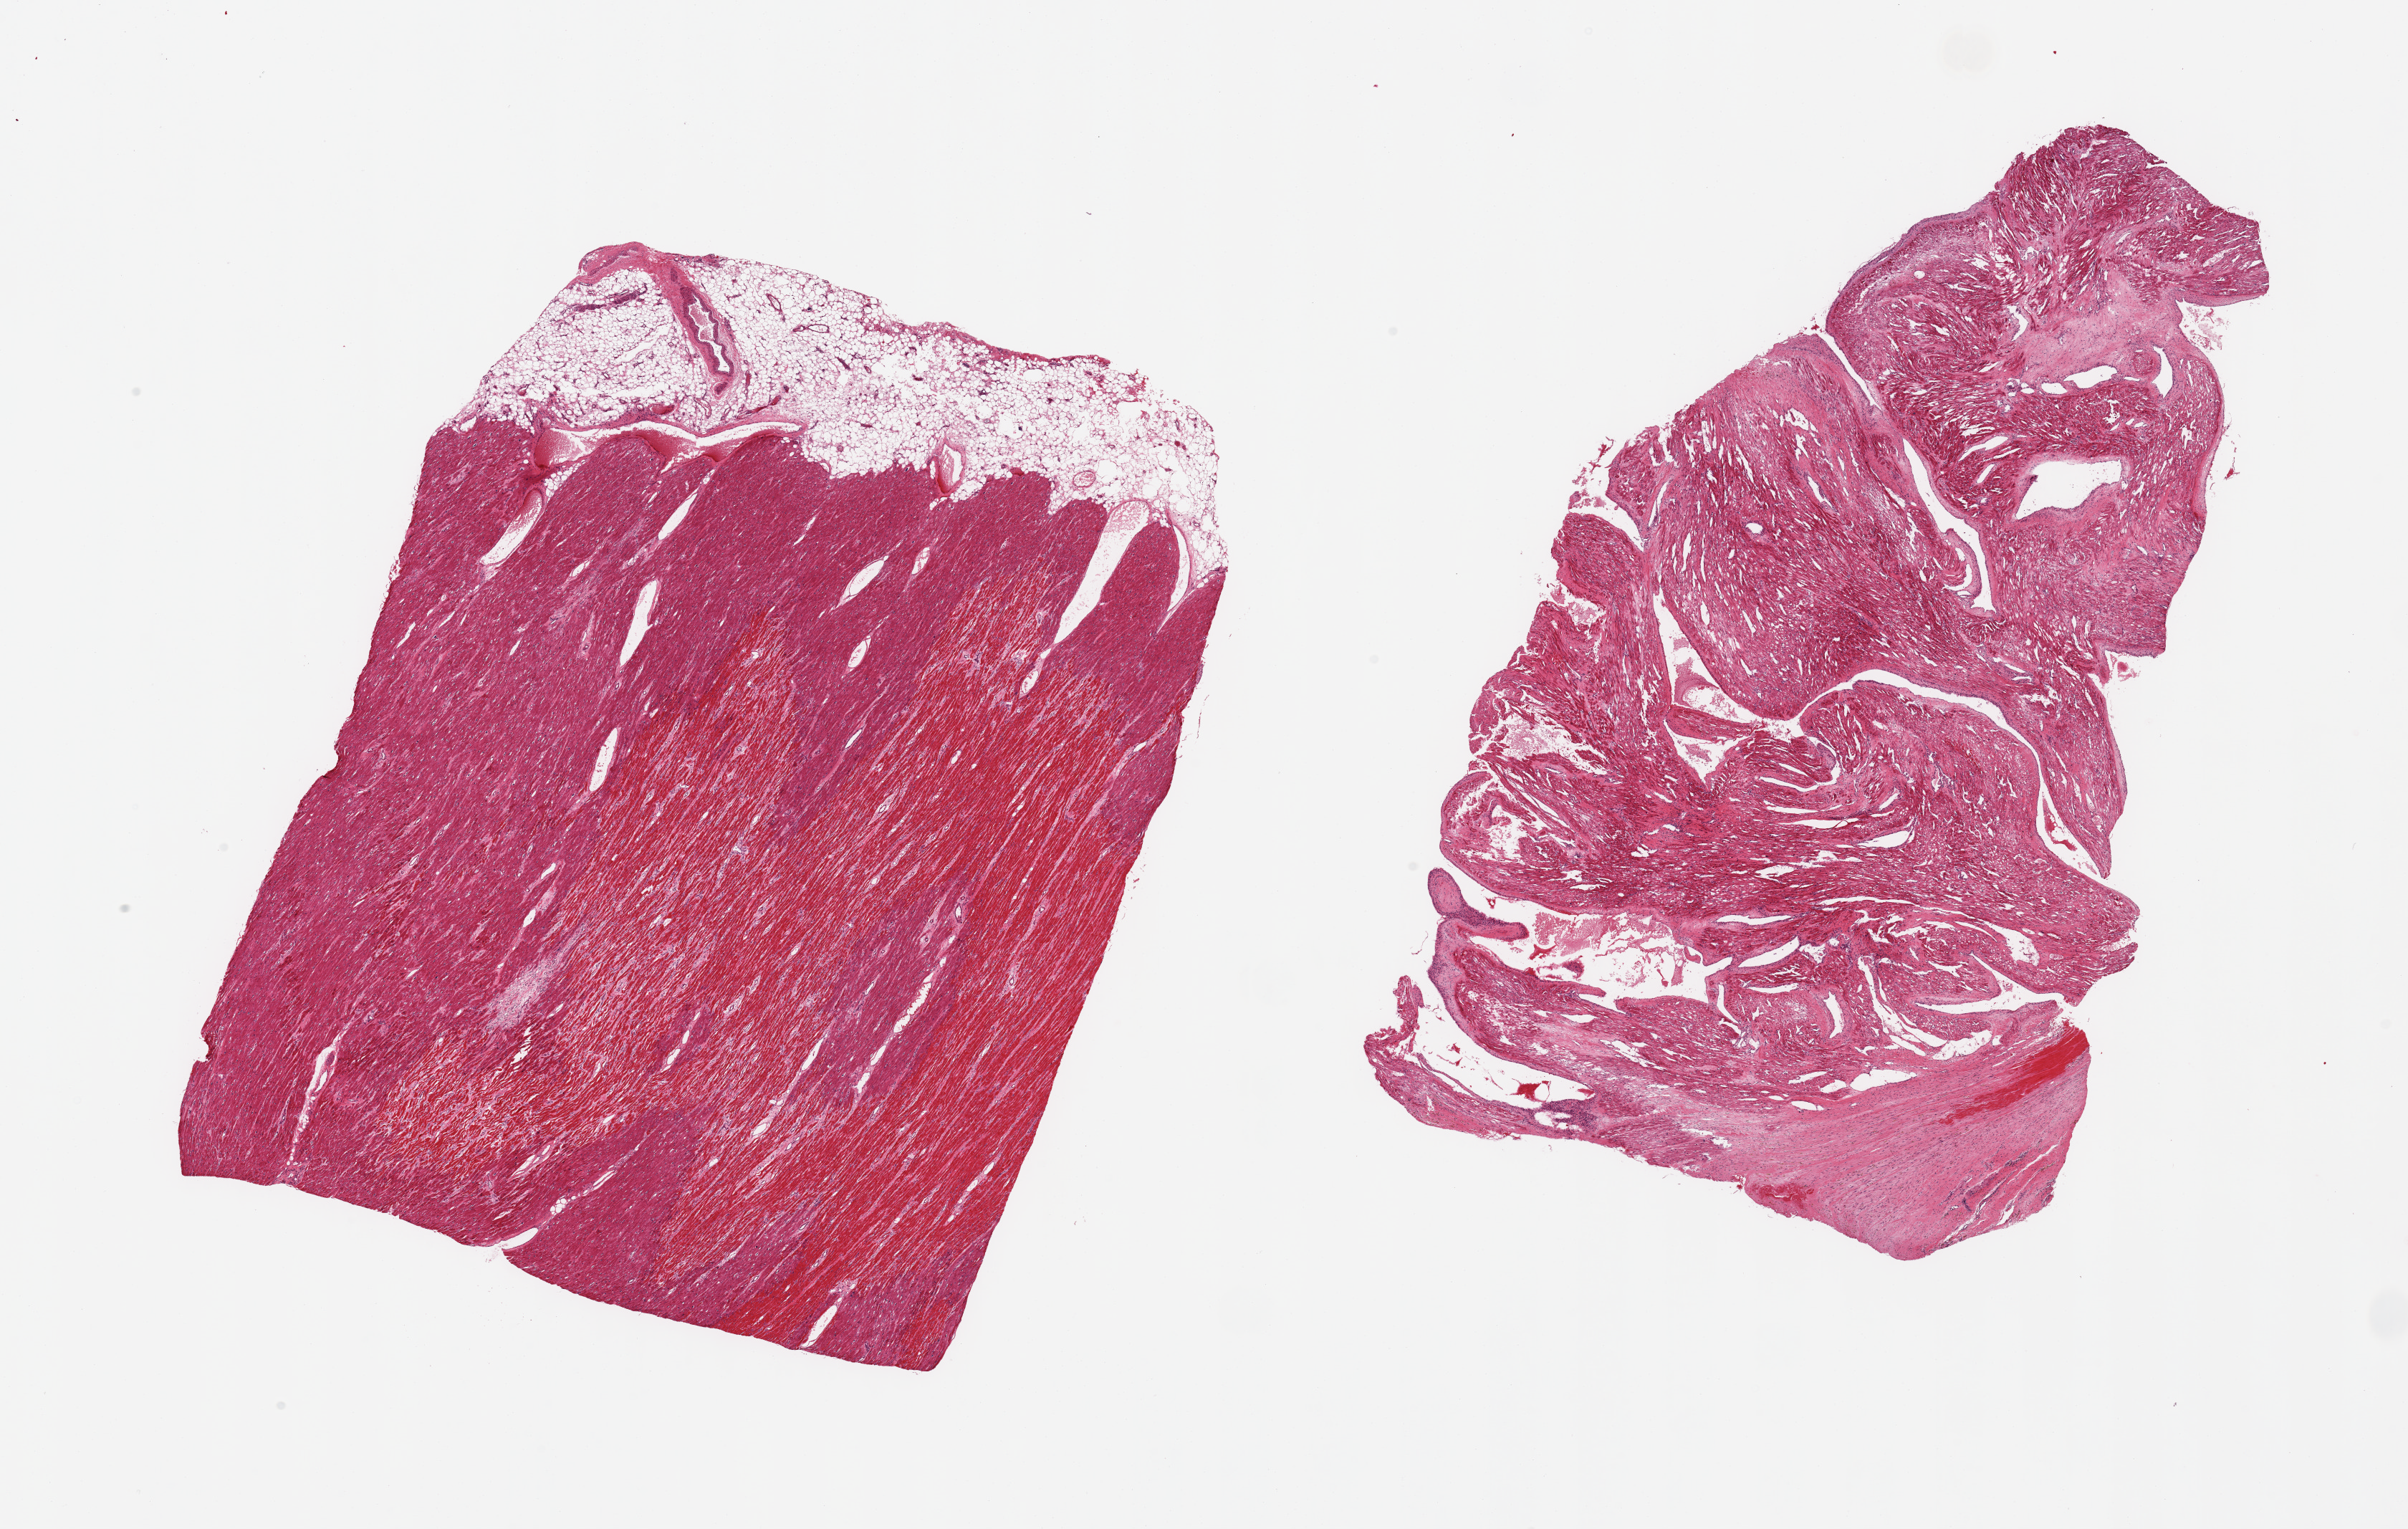
Digitized H&E-stained section, shown as a low-resolution overview of the whole scanned area (about 26.6 x 16.9 mm); PAXgene-fixed, paraffin-embedded tissue; sampled site (target tissue): heart; tissue donor sample. Donor sex: female.
Pathologist's review note for this sample: 2 pieces, patchy chronic and subacute ischemic damage/infarcts.